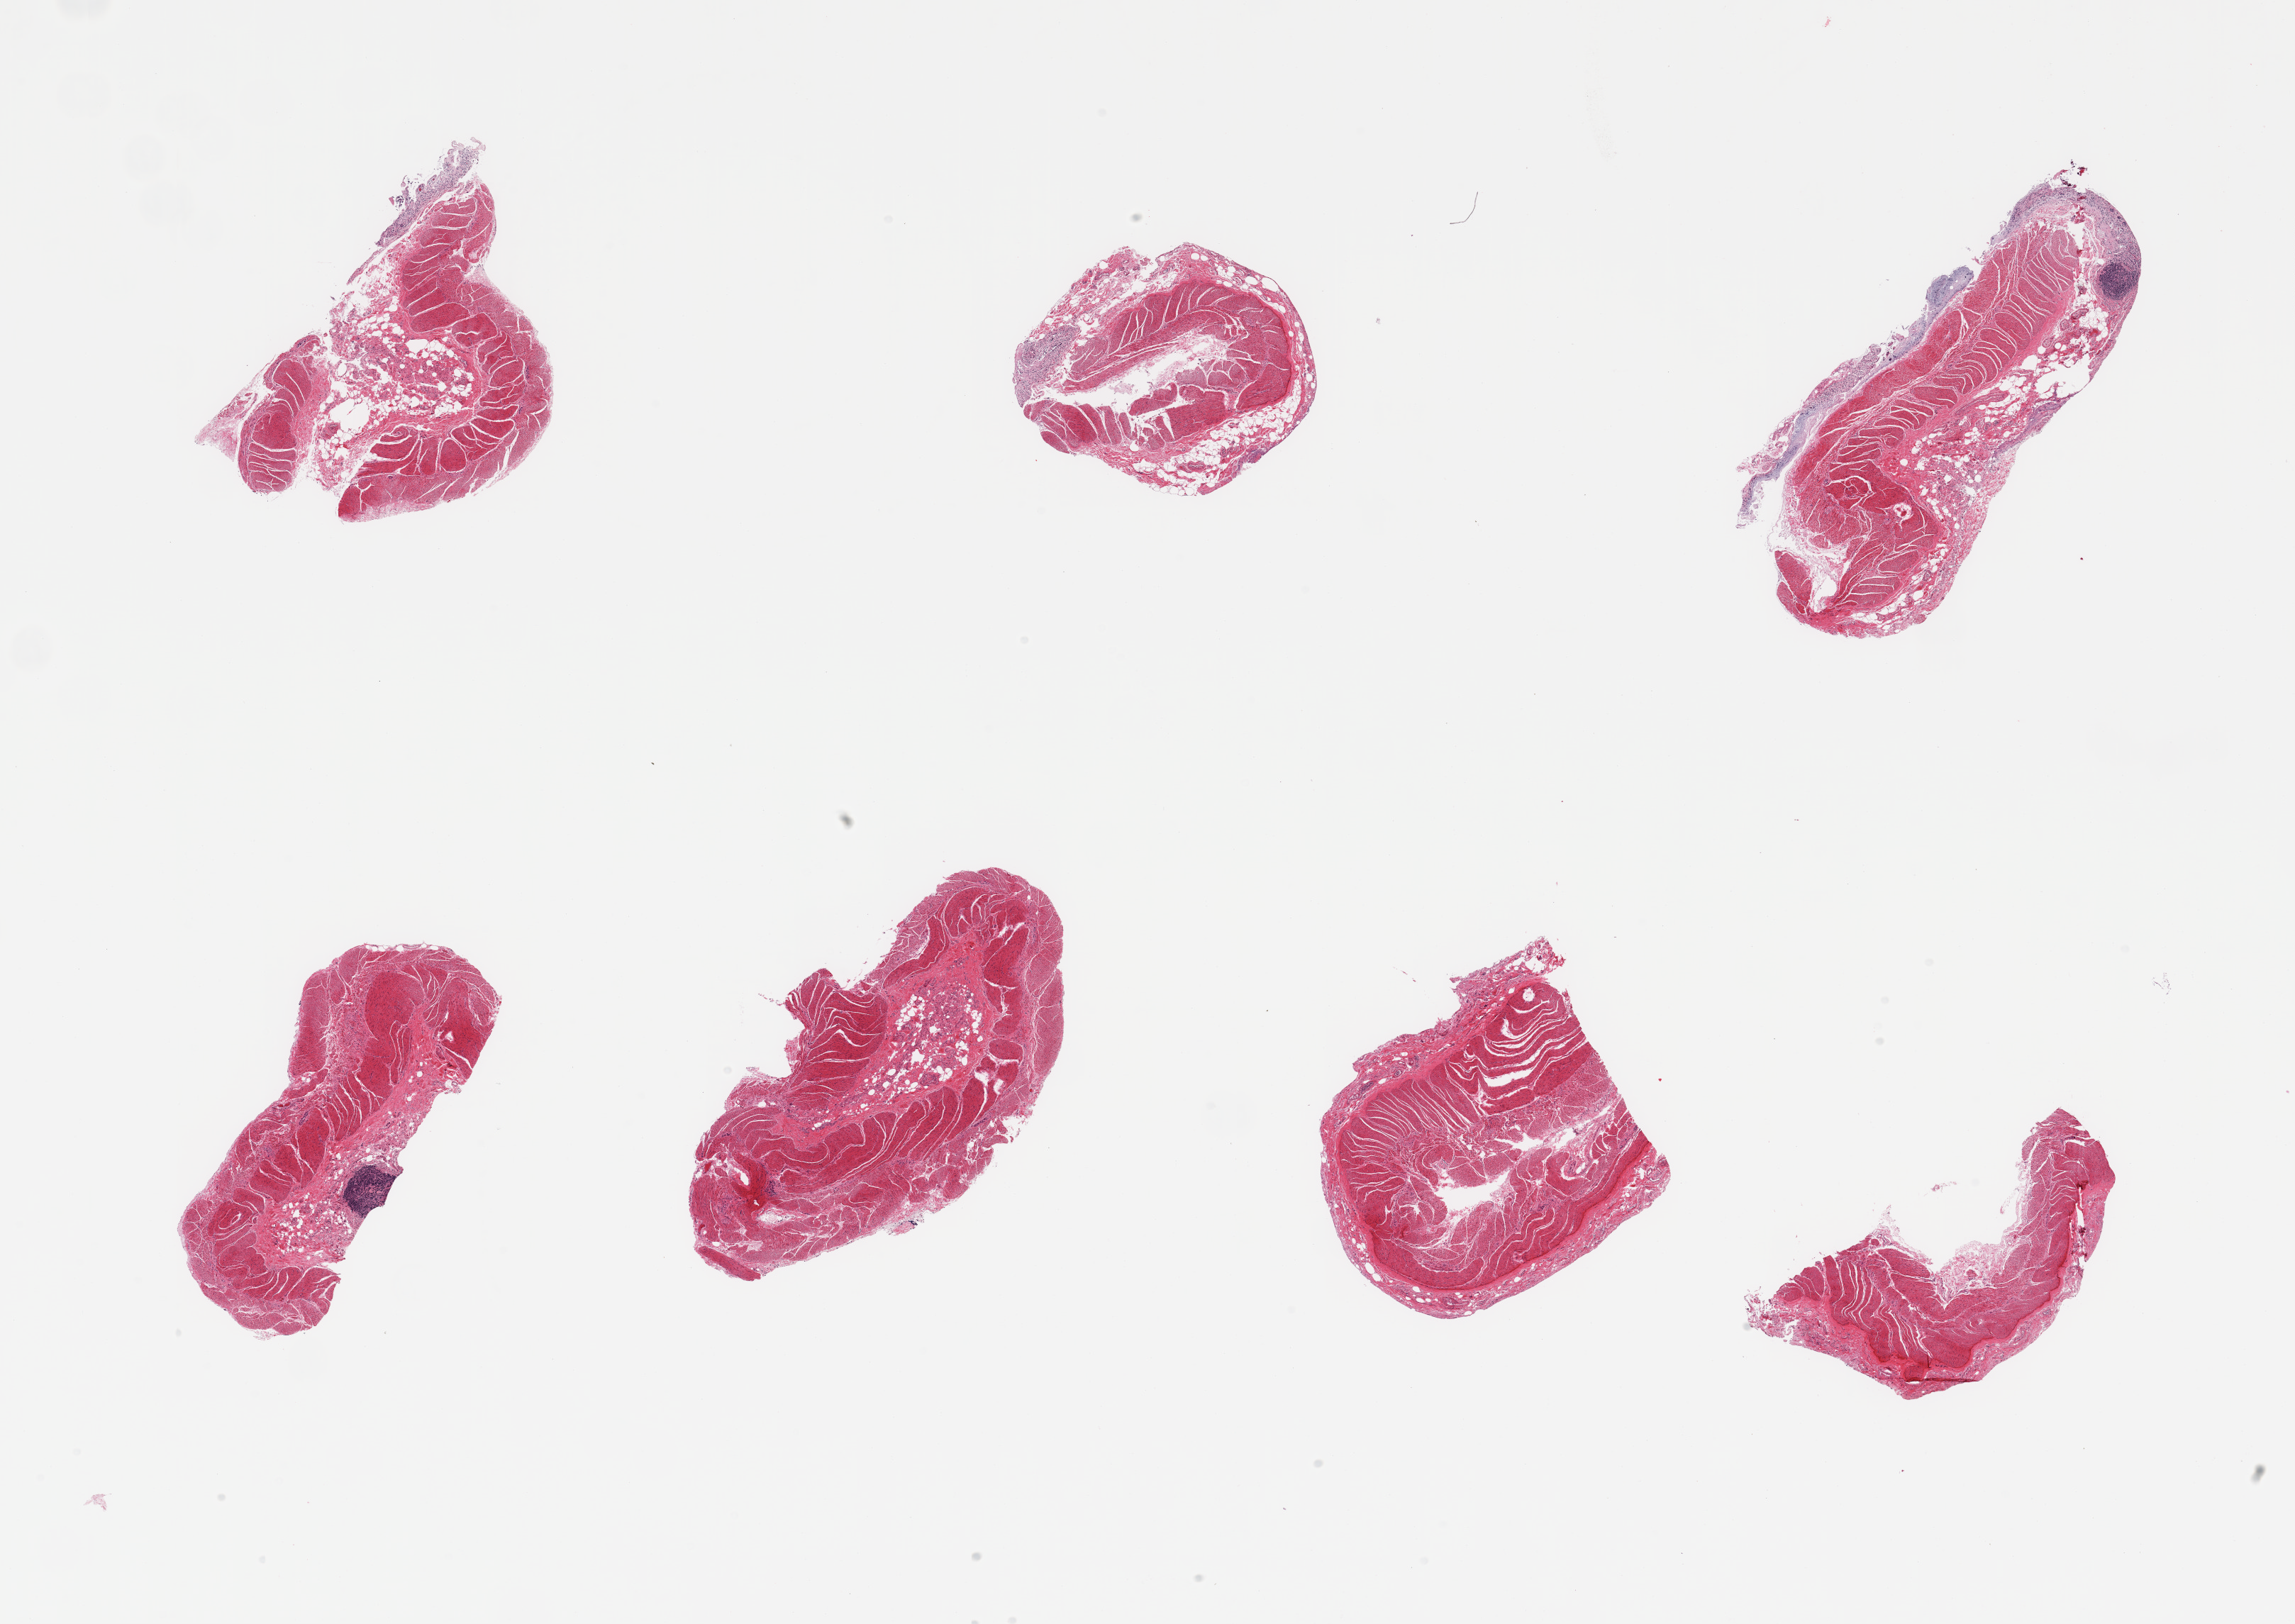
Haematoxylin and eosin whole-slide image, brightfield, shown as a low-resolution overview of the whole scanned area (about 25.6 x 18.1 mm, from a 20x scan); PAXgene-fixed, paraffin-embedded tissue; sampled site (target tissue): ileum; donor tissue sample. Donor sex: male.
Pathologist's review note for this sample: 6 pieces, mucosa autolyzed; target lymphoid aggregates less than 5% of tissue.